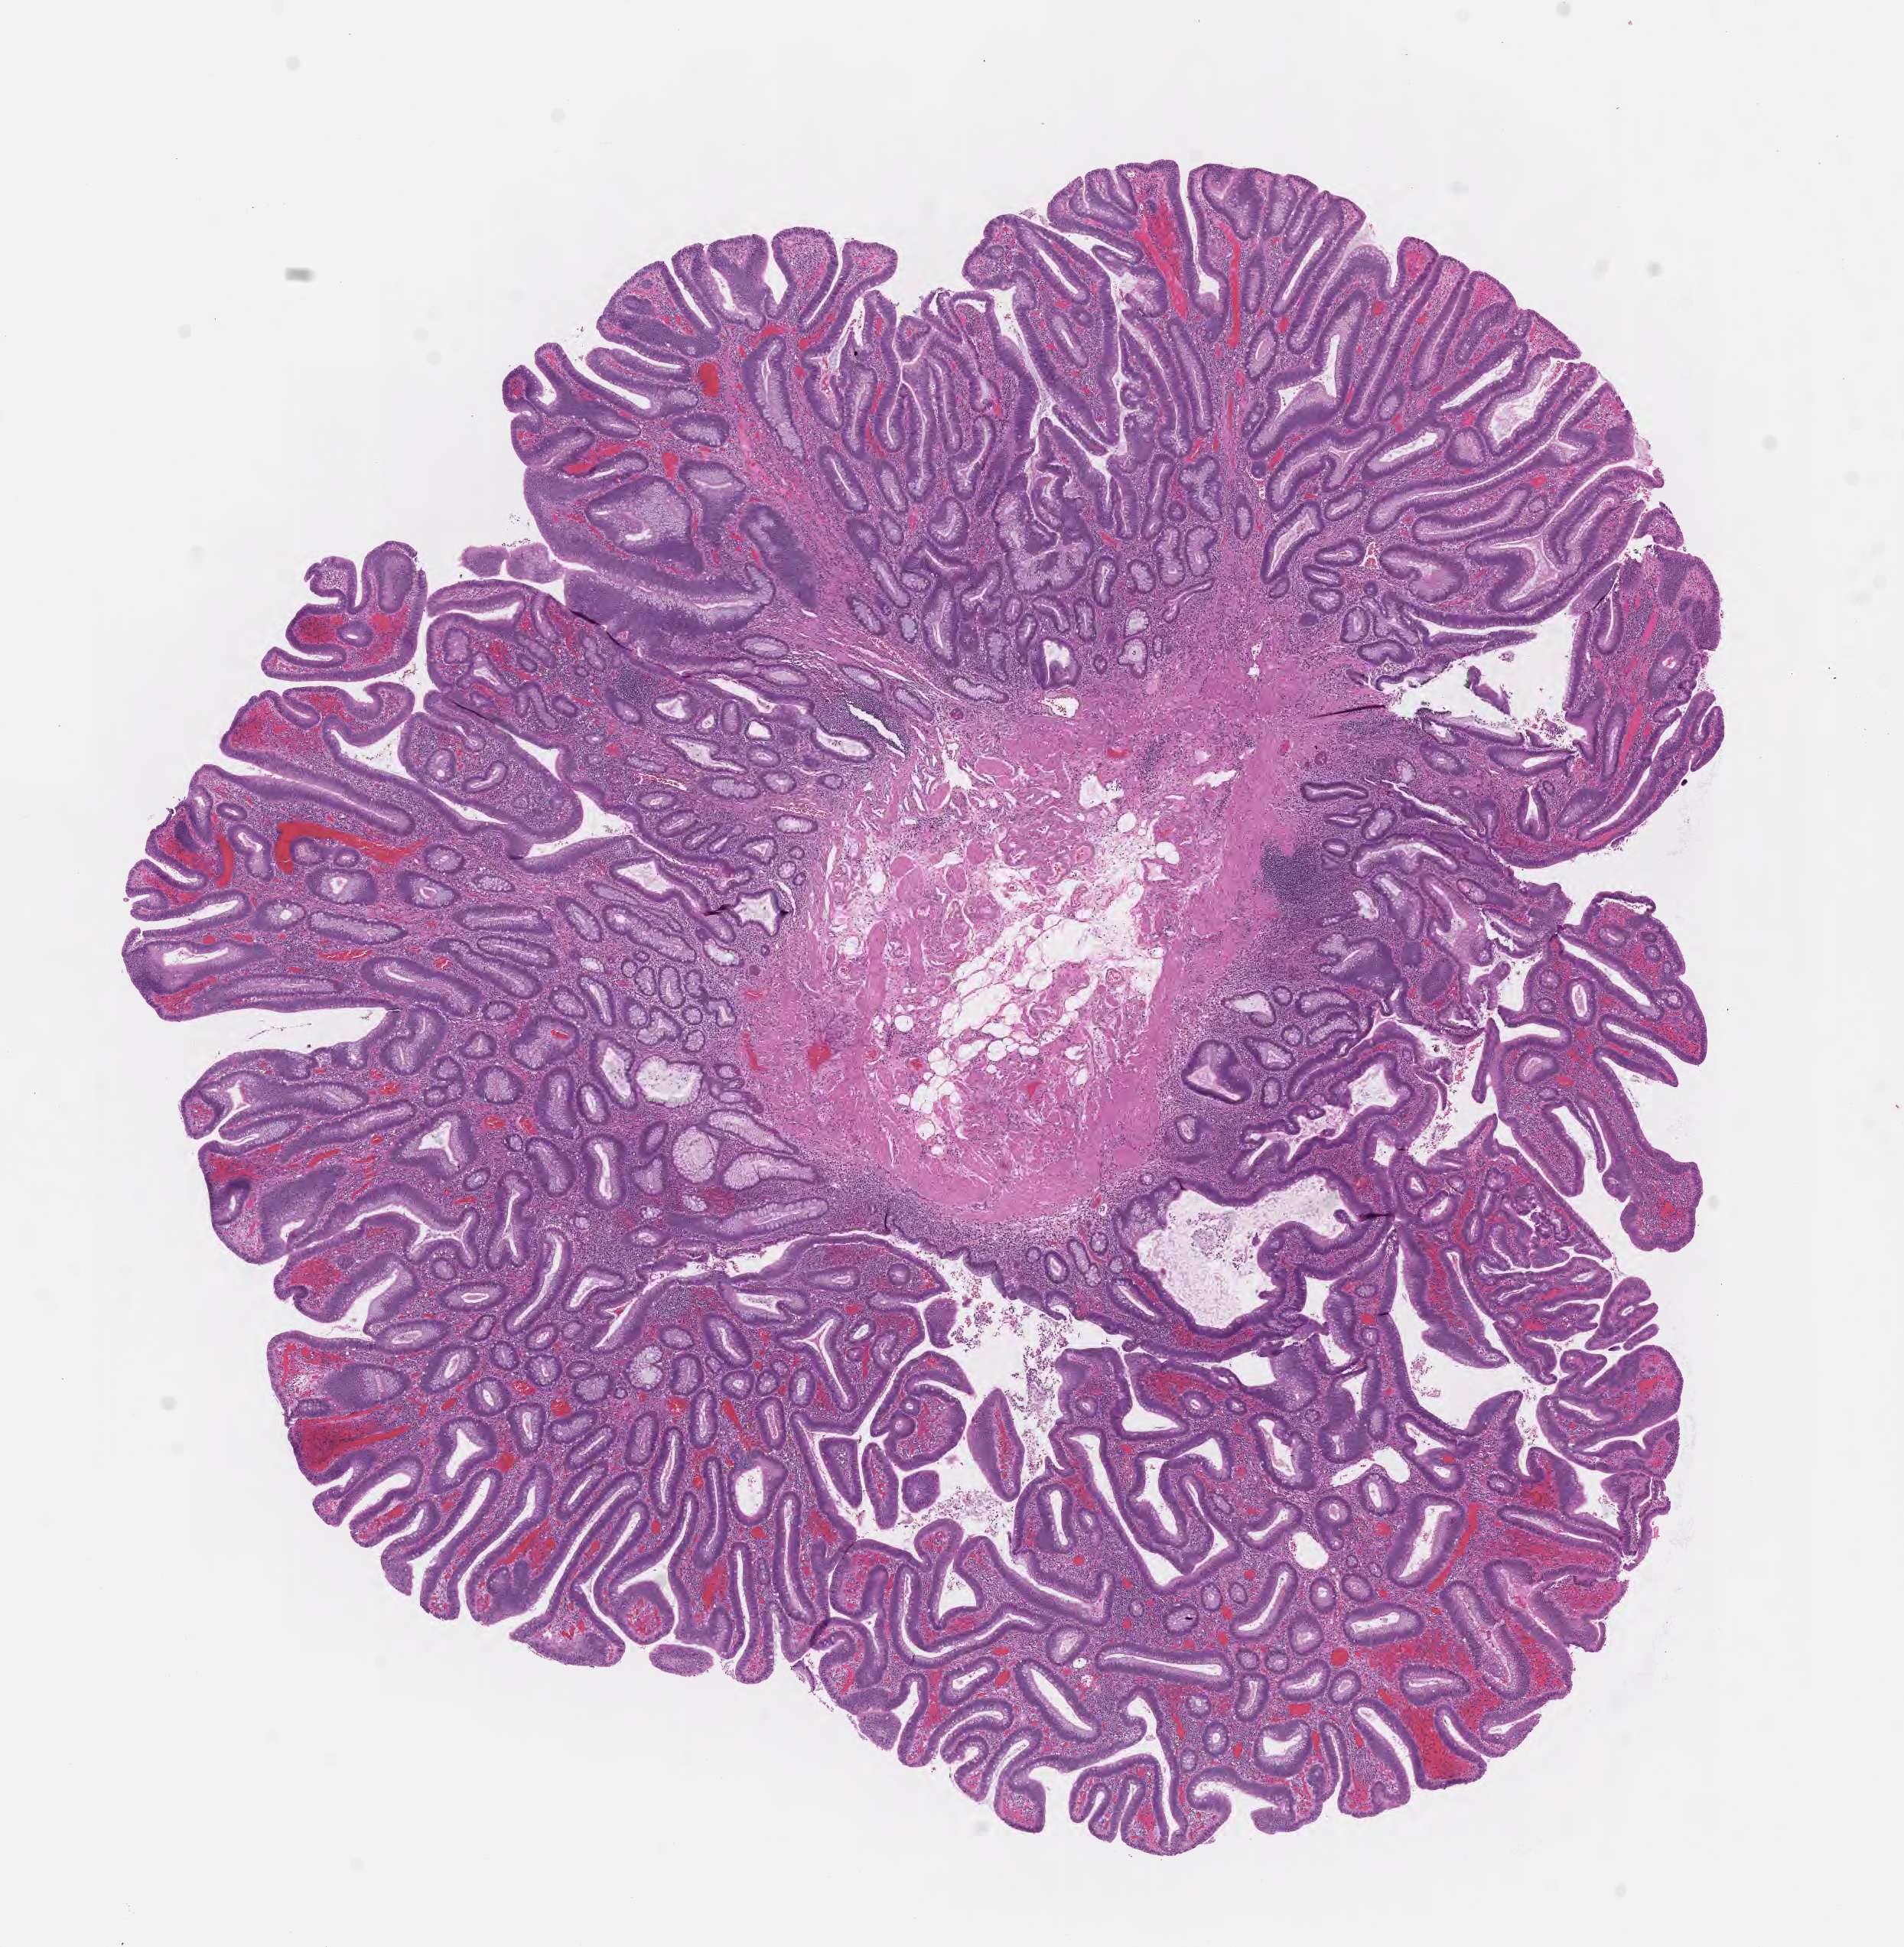
Digitized haematoxylin and eosin-stained section, low-resolution overview of the scanned area, about 10.1 x 10.3 mm; FFPE section; specimen: premalignant lesion from a patient with tubulovillous adenoma, NOS; site: cecum. Male, age 51 years at initial diagnosis. Composition of this section per pathologist review: tumor cells 80%, tumor nuclei 80%, stromal cells 20%, necrosis 0%, normal cells 0%. Inflammatory infiltration, as recorded: lymphocyte infiltration 5%, monocyte infiltration 3%, neutrophil infiltration 7%.
- this section: sample classed premalignant; the patient's recorded diagnosis is given above